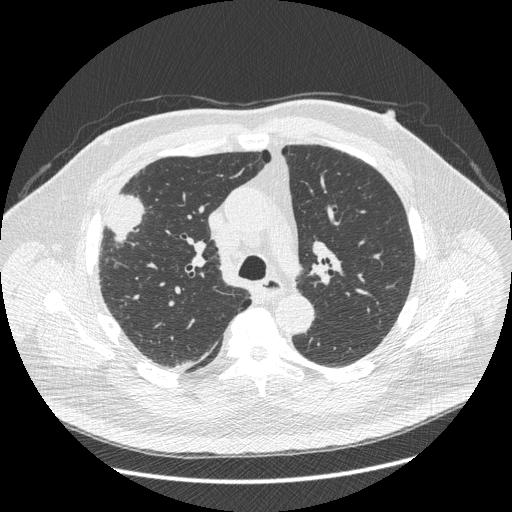
Low-dose screening chest CT, one axial slice. Slice 285 of 426 in the series (ordered by position). Reconstruction kernel STANDARD. 120 kVp. Lung window (W 1500 / L -600 HU). 512 × 512 image matrix.
Structures marked on this image (manually delineated by an expert):
- lesion 1 (tumor, upper lobe of right lung): bounding box (x1, y1, x2, y2) in pixels: (106, 195, 143, 236)